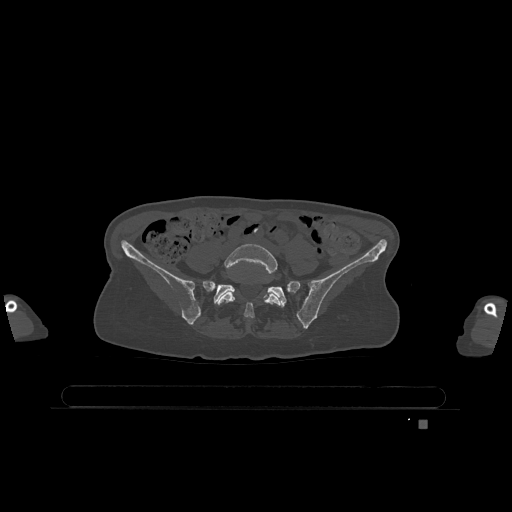
CT including the spine, one axial slice; slice 219 of 1317 in the series (ordered by position); bone window (W 1800 / L 400 HU); 0.5 mm slice thickness; 512 × 512 image matrix. Patient: female, 74 years. From the clinical record (not read from this slice): primary cancer: lung; vertebrae with lytic lesions (as recorded): T1, T4, T5, T6, L4, L5.
Structures marked on this image (semi-automatic segmentation, software-assisted and operator-edited):
- L5 vertebra: bounding box <216,244,281,318> (left, top, right, bottom; pixels)